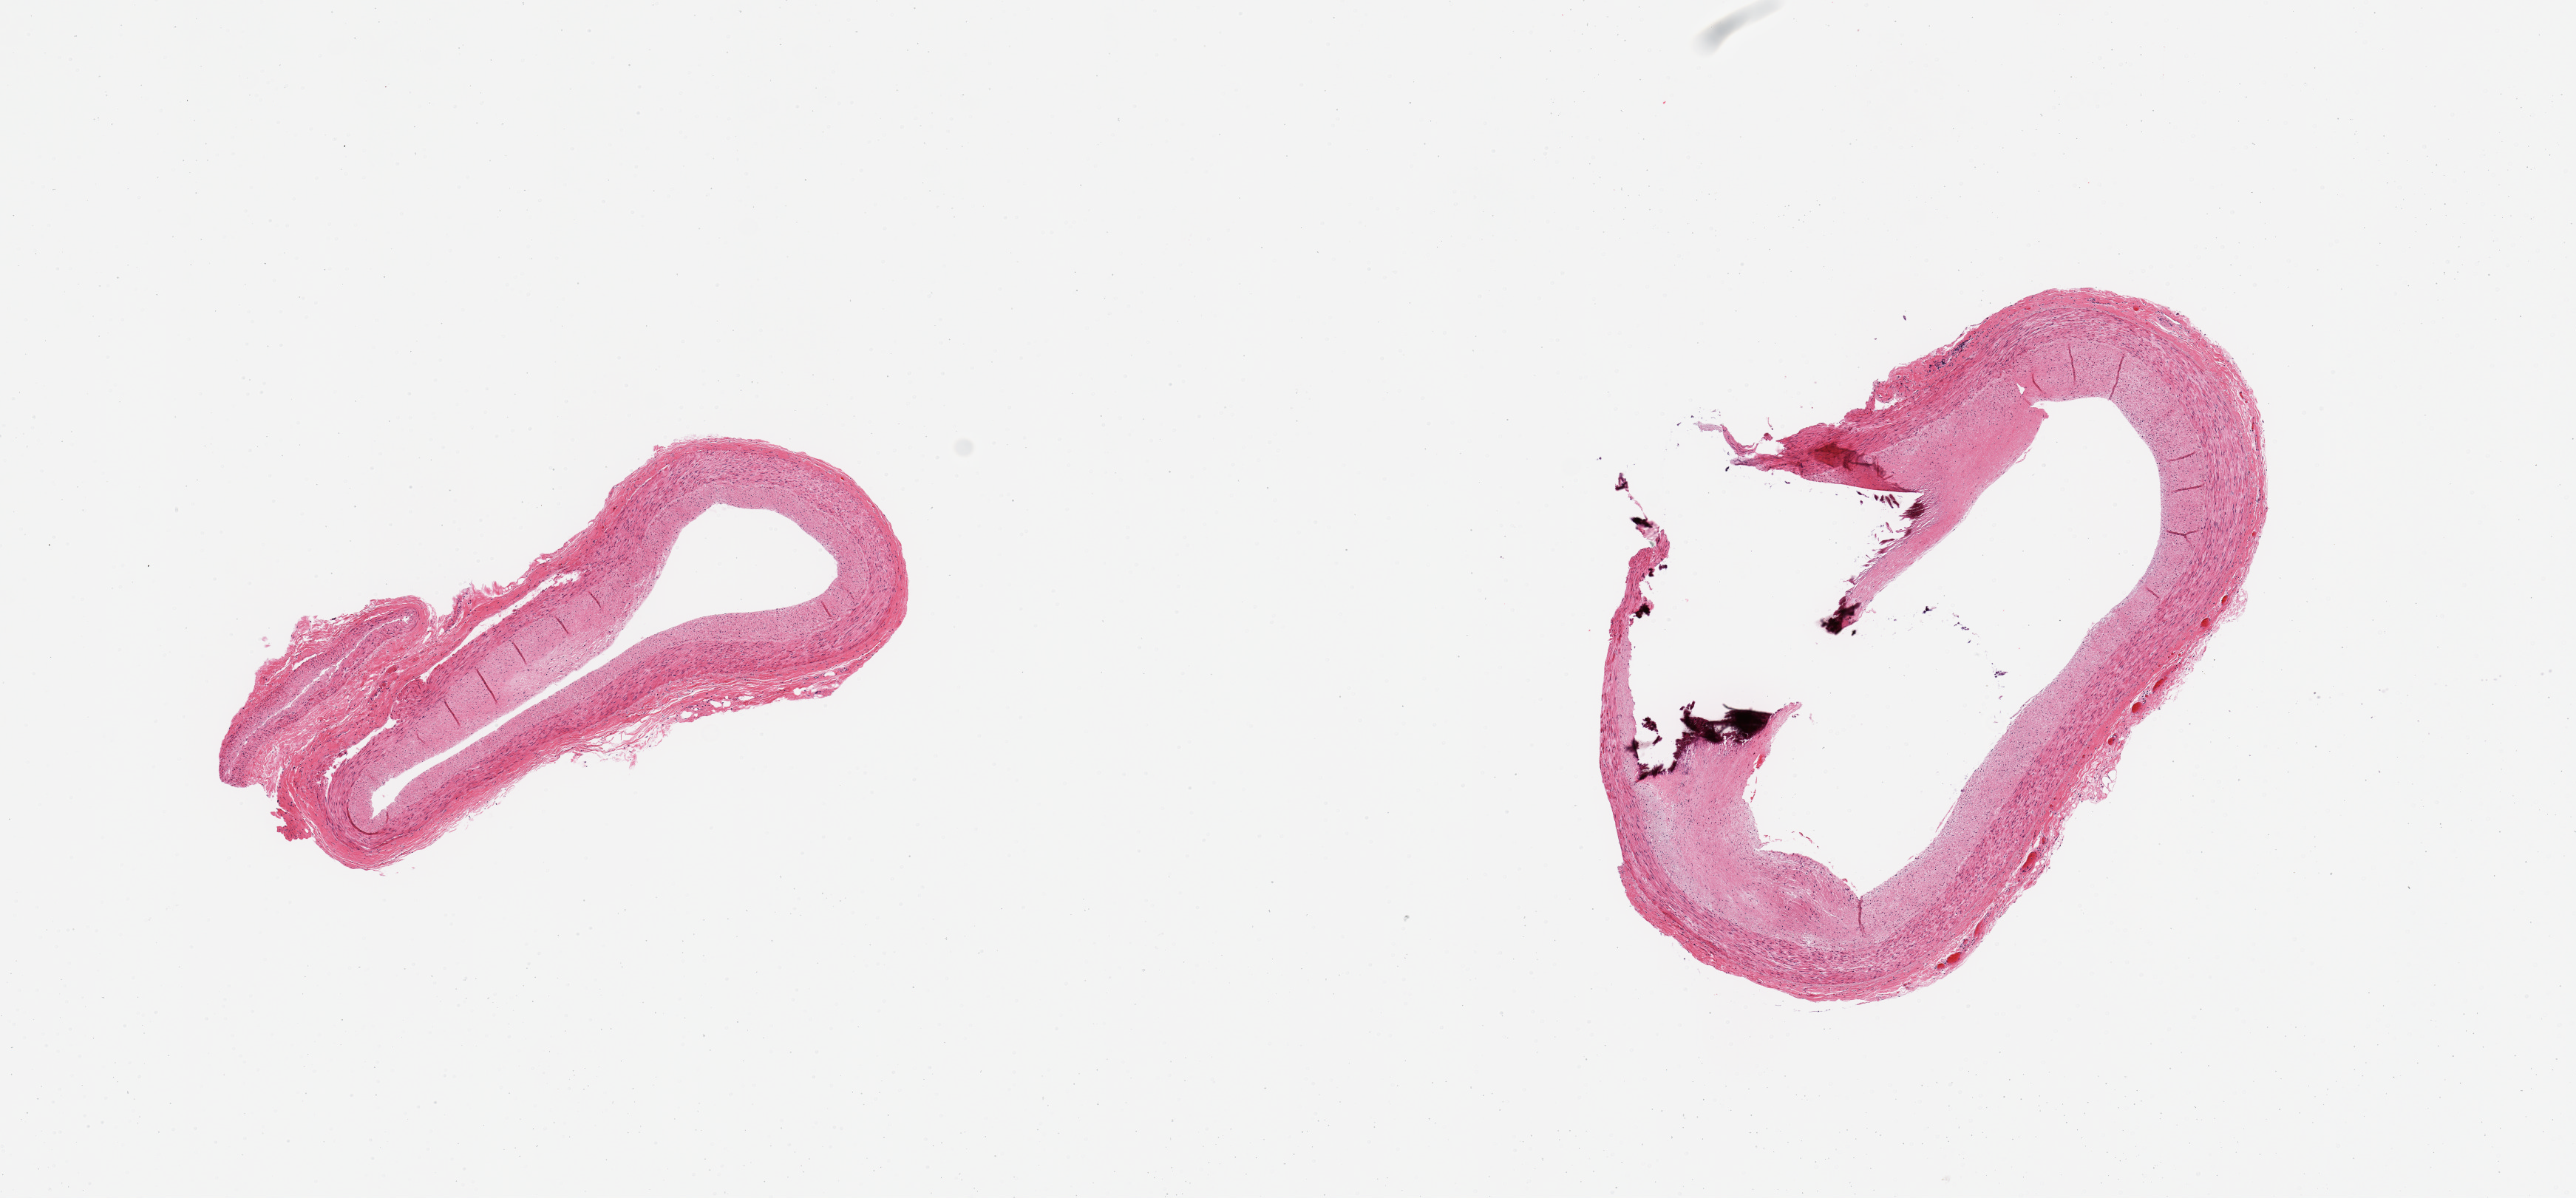
Digitized hematoxylin and eosin (H&E)-stained section, brightfield — a low-resolution overview of the entire scanned area, about 13.8 x 6.4 mm (slide scanned at 20x), PAXgene-fixed paraffin-embedded (PFPE) section, section of coronary artery (target tissue), tissue donor sample.
Pathologist's review note for this sample: 2 pieces; slight plaque, but large calcific focus, 1 mm.